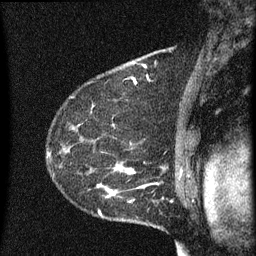
Breast MRI (dynamic contrast-enhanced), one sagittal slice; position 45 of 60 along the scan axis; dynamic contrast-enhanced series, image 2 of 3 at this slice position (ordered by acquisition); 1.5 T; TE 4.2 ms, TR 8 ms; 2 mm slice thickness; 256 × 256 image matrix, field of view 180 × 180 mm. Patient: female, 55 years.
Annotated regions visible in this slice (semi-automatically segmented with operator editing):
- analysis volume of interest (the breast-tissue region the enhancement analysis was run in; not a lesion): bounding box (x1, y1, x2, y2) in pixels: (51, 156, 145, 217)
- tumour enhancement mask (voxels above the 70 % enhancement threshold inside the analysis volume of interest): (97, 164, 145, 217)